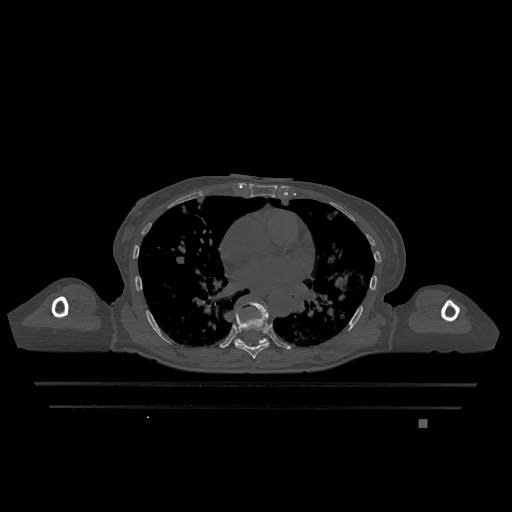
CT including the spine, one axial slice; position 725 of 1317 along the scan axis; bone window (W 1800 / L 400 HU); 0.5 mm slice thickness; 512 × 512 image matrix, field of view 500 × 500 mm. Patient: female, 74 years. Case-level facts recorded for this patient, not image findings: primary cancer: lung; vertebrae with lytic lesions (as recorded): T1, T4, T5, T6, L4, L5.
Annotated regions visible in this slice (semi-automatically segmented with operator editing):
- T7 vertebra: box from (x=234, y=302) to (x=270, y=359) px
- T9 vertebra: (x=235, y=338)–(x=268, y=345)